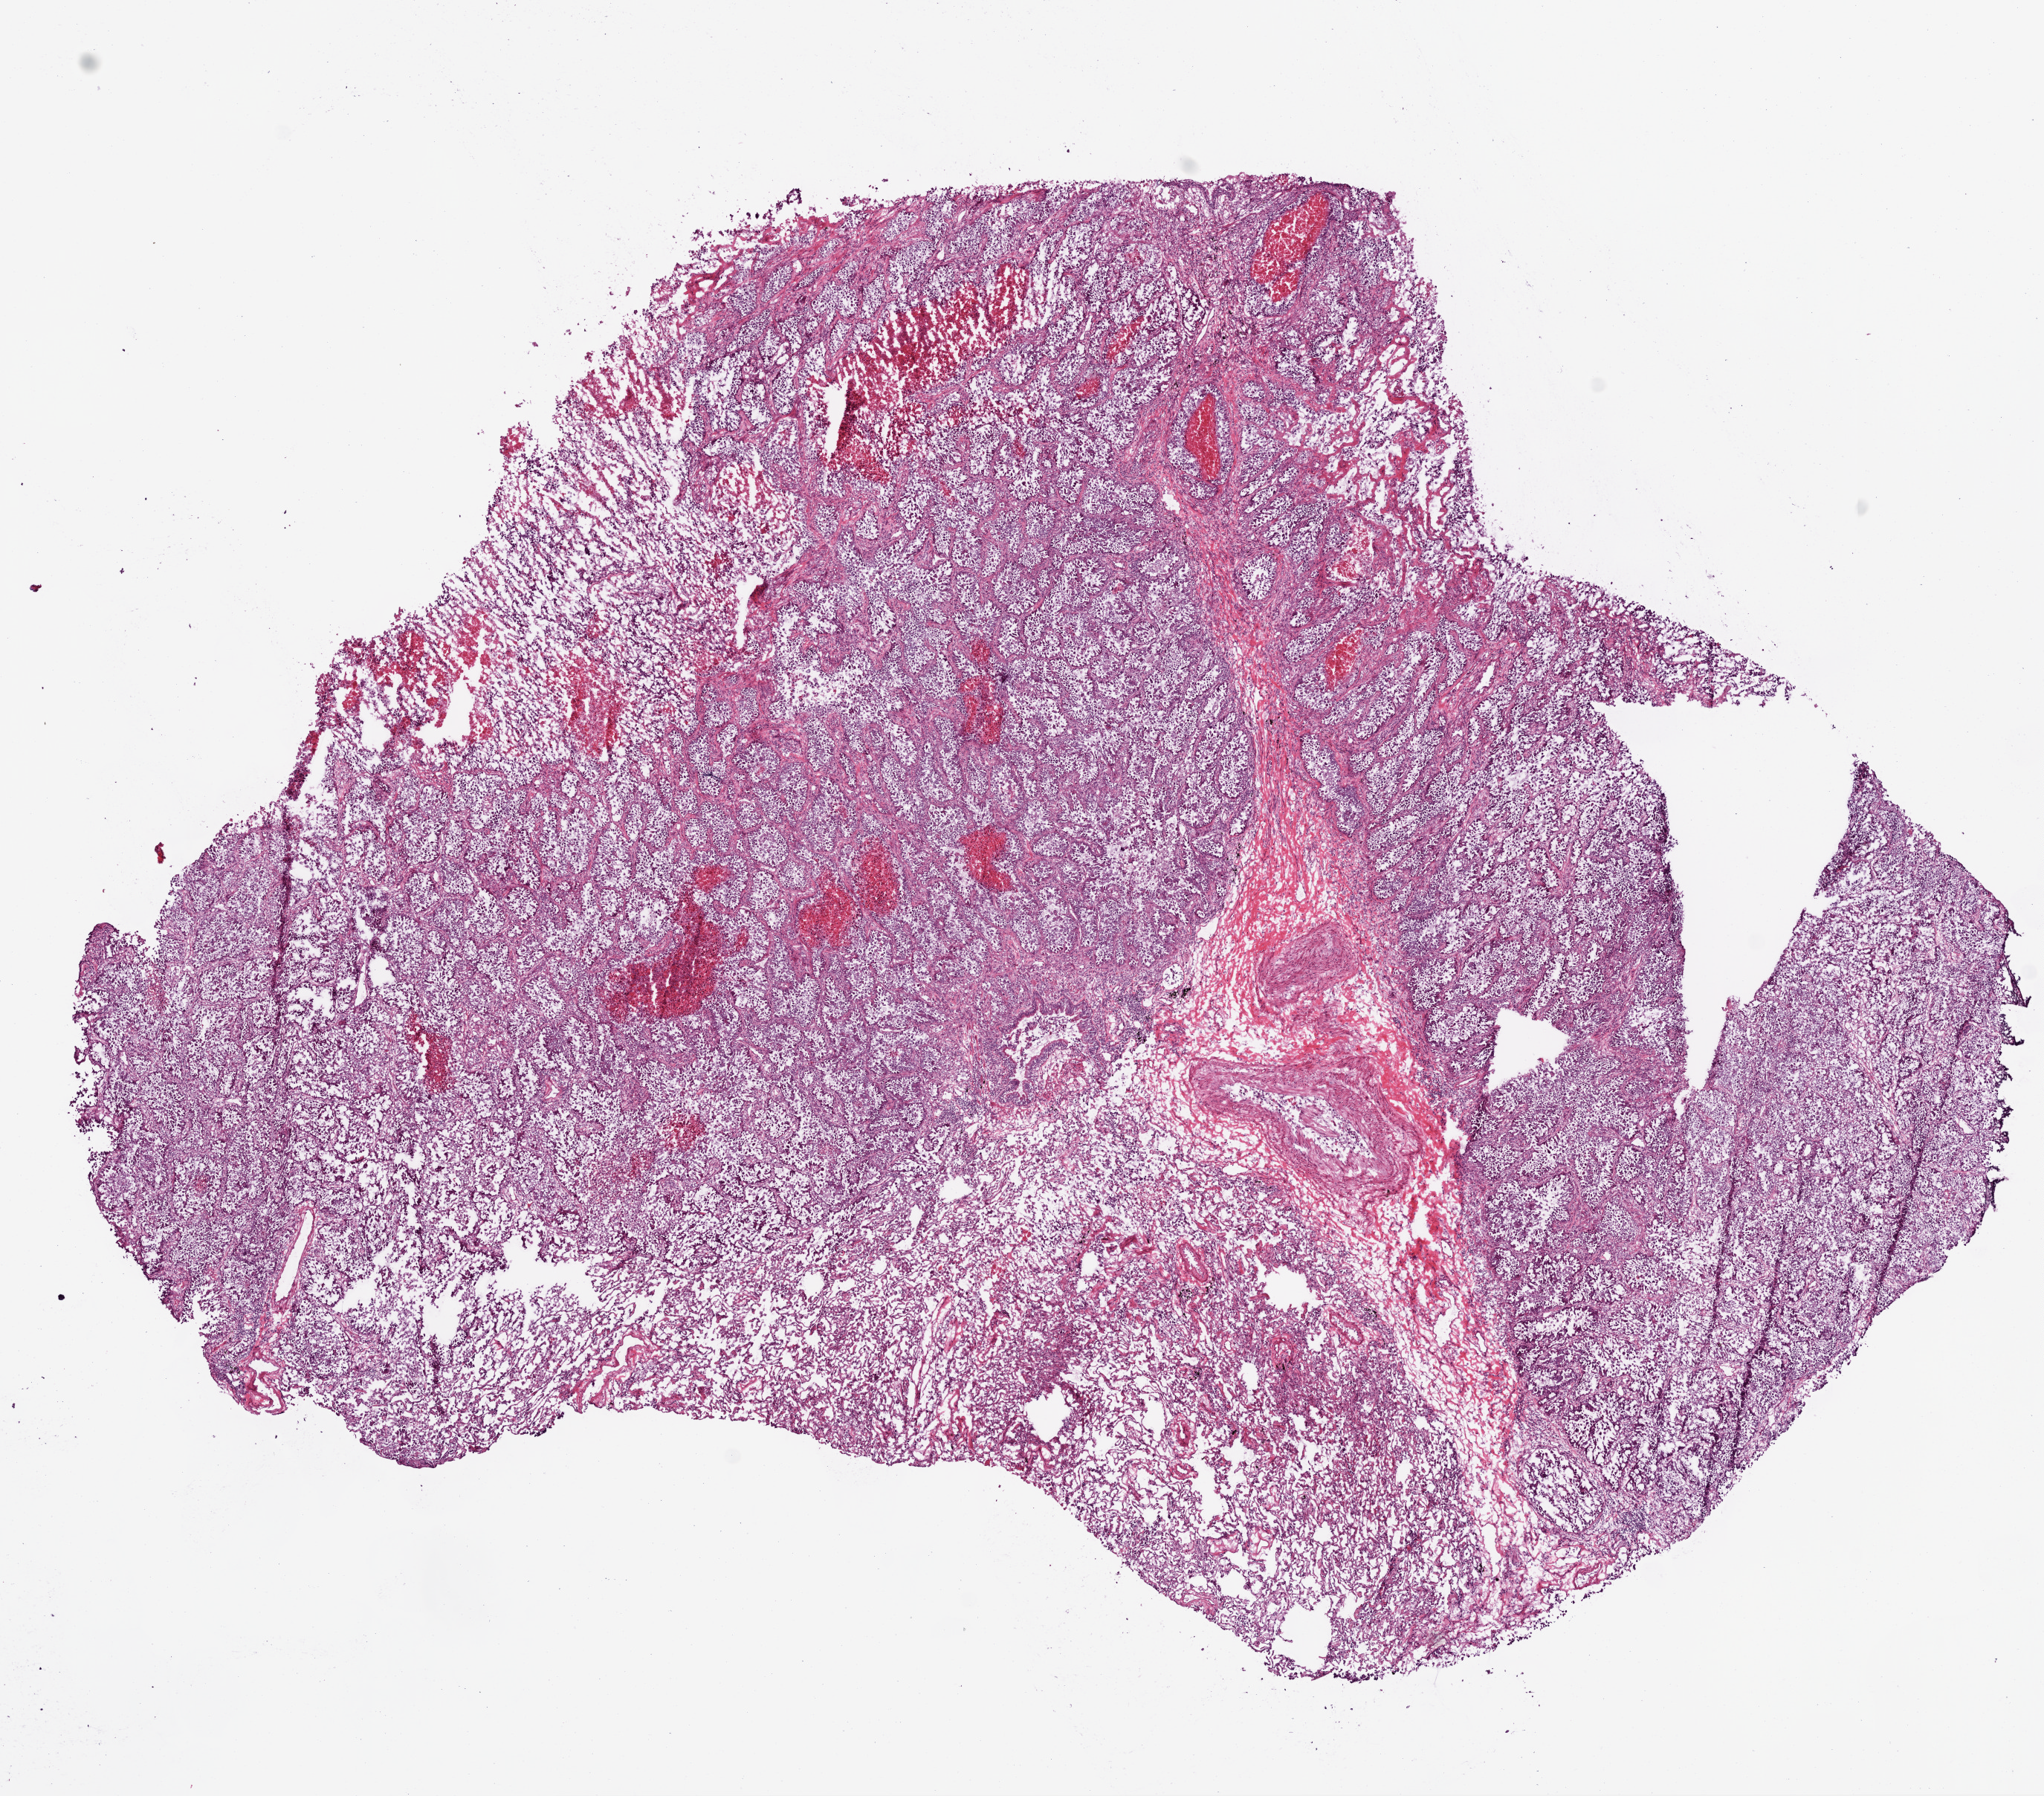
H&E-stained whole-slide image, shown as a low-resolution overview of the whole scanned area (about 11.0 x 9.7 mm, from a 20x scan), frozen section from the bottom of the tissue portion, lung, primary tumour sample. Patient: male, age at initial diagnosis 70 years. Pathologist review of this section (percent, as recorded): tumour cells 60%, tumour nuclei 80%, normal cells 15%, stromal cells 20%, necrosis 5%.
Pathologic diagnosis: Adenocarcinoma, NOS (lower lobe, lung). AJCC pathologic stage: IV (6th edition). Laterality: right. TNM: T2 N2 M1.